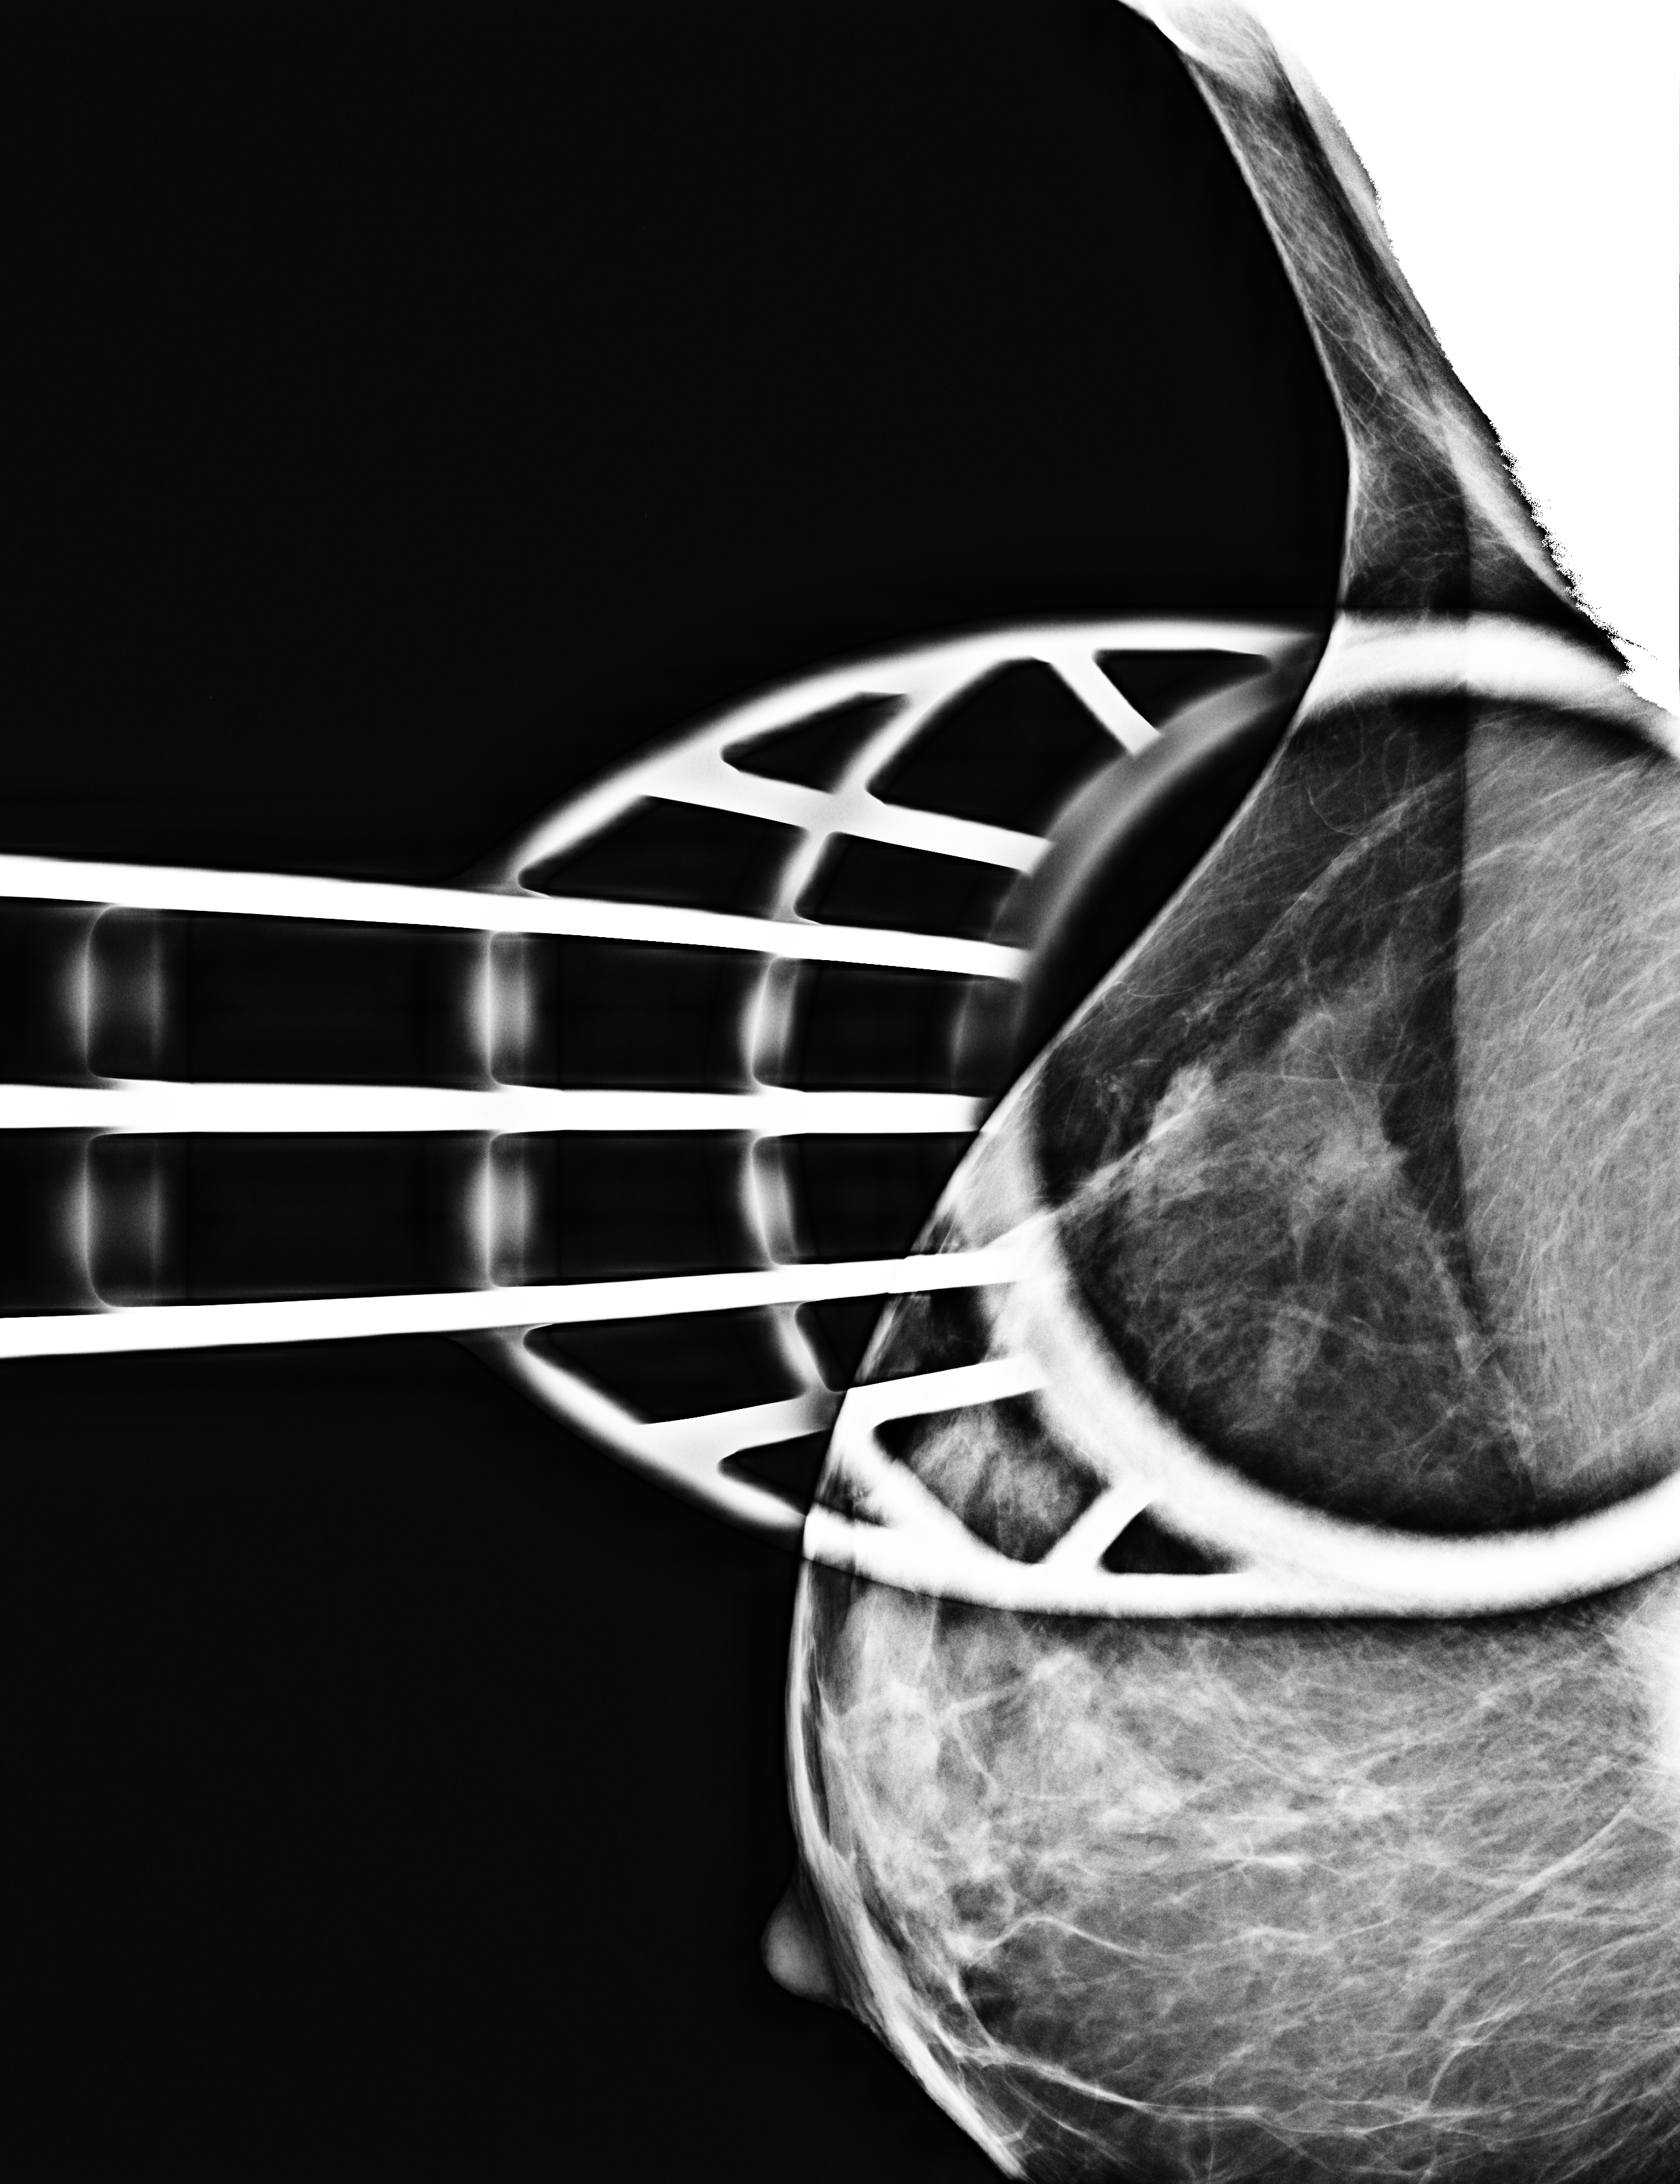
Additional work-up view; compressed breast thickness 34 mm.
Image type: full-field digital mammogram. Breast: right. Projection: laterally exaggerated craniocaudal (XCCL) view, spot compression.